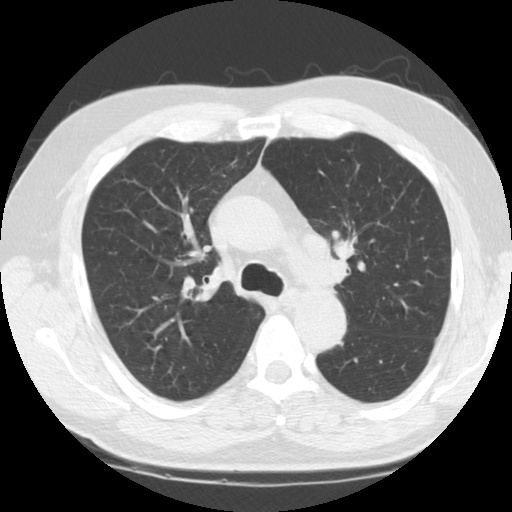
Chest CT (low-dose screening protocol), one axial image; third screening round (two years after baseline); lung window (W 1500 / L -600 HU); 120 kVp; slice 39 of 124 in the series. Male participant, aged 60 years at enrolment. Current smoker at enrolment.
• Expert-annotated lung lesion, bounding box [x1, y1, x2, y2] px = [315, 221, 369, 273].
• The exam's reader record, not a measurement of the box and not confirmed to be the same lesion: non-calcified nodule or mass ≥4 mm, left upper lobe, 24 × 21 mm, smooth margins, soft tissue attenuation, pre-existing on the prior screen: no.
• Official screen result: positive, other.
• Lung cancer was diagnosed 14 days after this screen: small cell carcinoma, NOS, left upper lobe, stage IIA (AJCC 6th edition), 26 mm at pathology.